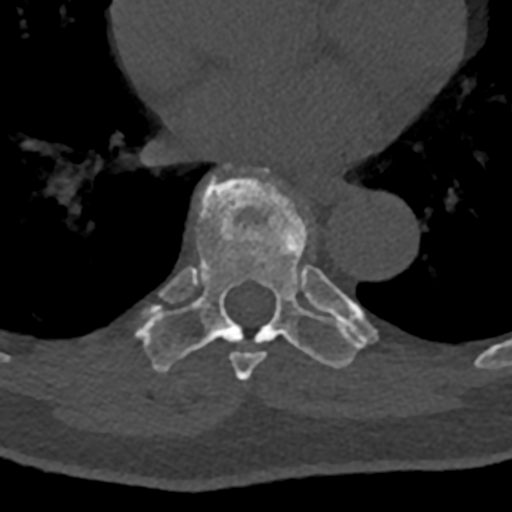
CT including the spine, one axial slice. Slice 726 of 797 in the series (ordered by position). Reconstruction kernel Br40s/3. Bone window (W 1800 / L 400 HU). 0.5 mm slice thickness. 512 × 512 image matrix. Patient: male, 74 years. From the clinical record (not read from this slice): primary cancer: renal; vertebrae with lytic lesions (as recorded): T10, L1, L2, L3, L4, L5.
Structures marked on this image (semi-automatic segmentation, software-assisted and operator-edited):
- T7 vertebra: bounding box <222,169,350,381> (left, top, right, bottom; pixels)
- T8 vertebra: <136,162,376,373>